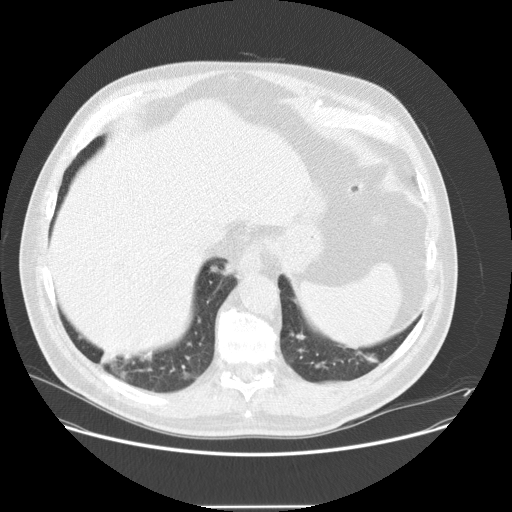
Low-dose screening chest CT, axial slice, first (baseline) screen, lung window (W 1500 / L -600 HU), 2.5 mm slice thickness, 120 kVp, slice 107 of 143 in the series. Male, age 61 years at enrolment. Current smoker at enrolment.
• 3 lesions marked by an expert reader on this slice (largest first), bounding box [x1, y1, x2, y2] px = [91, 339, 146, 389]; [199, 251, 243, 292]; [166, 356, 206, 393].
• The screening reader recorded 2 non-calcified nodules or masses ≥4 mm on this exam; which of them these boxes mark is not recorded.
• Official screen result: positive, change unspecified: nodule(s) >= 4 mm or enlarging nodule(s), mass(es), or other non-specific abnormalities suspicious for lung cancer.
• Lung cancer was diagnosed 41 days after this screen: bronchiolo-alveolar carcinoma, mucinous, right lower lobe, well differentiated (G1), stage IV (AJCC 6th edition), 23 mm at pathology.